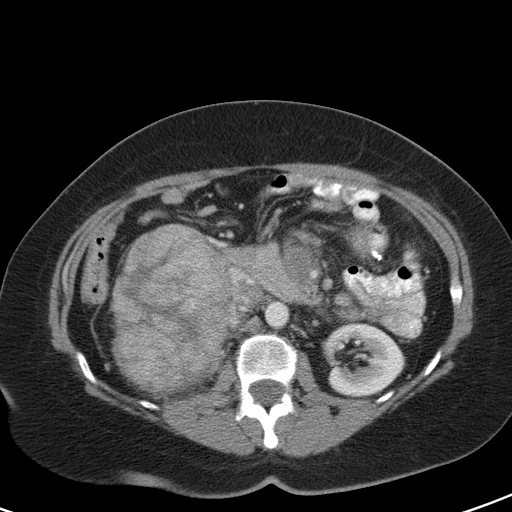
Contrast-enhanced abdominal CT, one axial slice; slice 62 of 126 in the series (ordered by position); 120 kVp; intravenous contrast given; soft-tissue window (W 400 / L 40 HU); 512 × 512 image matrix, field of view 356 × 356 mm. Female patient, age 51 years. From the clinical record (not read from this slice): diagnosis: adrenocortical carcinoma; tumour side: right adrenal; tumour size at pathology: 17 cm; Ki-67 index: 12 %; stage (as recorded): 2.
Structures marked on this image (semi-automatically segmented with operator editing):
- mass: bounding box [x1, y1, x2, y2] px = [115, 224, 229, 393]